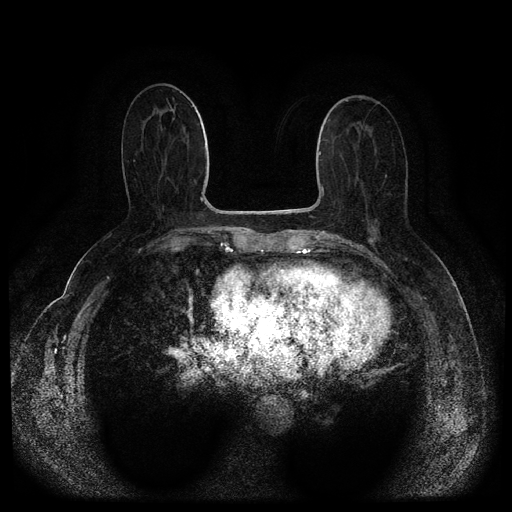
Breast MRI (dynamic contrast-enhanced, multi-phase), one axial slice; slice 43 of 116 in the series (ordered by position); dynamic contrast-enhanced series, time point 2 of 5 at this slice position (early post-contrast); 1.5 T; TE 2.6 ms, TR 5.4 ms; 512 × 512 image matrix, field of view 340 × 340 mm. Female patient, age 67 years.
Outlined on this slice (semi-automatic segmentation, software-assisted and operator-edited):
- breast lesion (labelled 'tumour' in the annotation; benign lesions carry a separate 'benign' label): bounding box (x1, y1, x2, y2) in pixels: (368, 235, 375, 245)